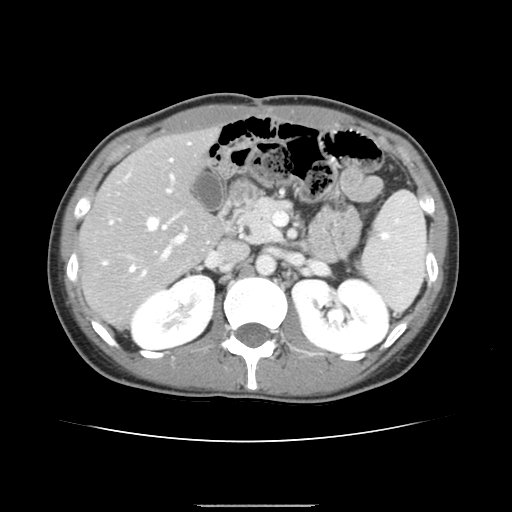
Contrast-enhanced abdominal CT, one axial slice. Position 82 of 150 along the scan axis. Intravenous contrast given. Soft-tissue window (W 400 / L 40 HU). 2.5 mm slice thickness. 512 × 512 image matrix, field of view 324 × 324 mm. Female patient, age 32 years. Case-level facts recorded for this patient, not image findings: diagnosis: colorectal cancer liver metastases, imaged before liver resection; multiple liver metastases: yes.
Outlined on this slice (expert manual segmentation):
- hepatic veins: bounding box [x1, y1, x2, y2] px = [104, 159, 172, 271]
- liver: [80, 130, 222, 325]
- planned liver remnant (the part of the liver to remain after resection): [80, 130, 221, 276]
- portal vein (with intrahepatic branches): [127, 174, 187, 276]